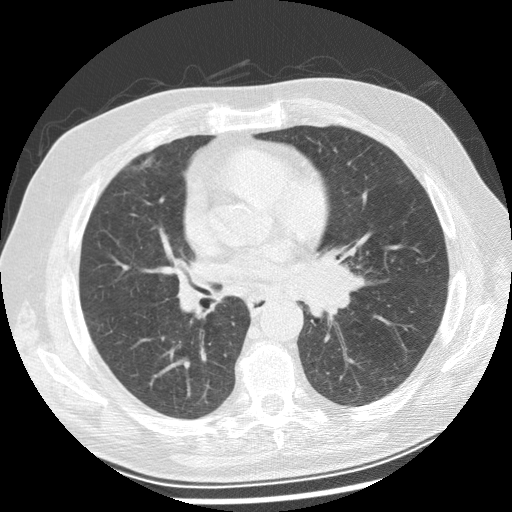
Chest CT (low-dose screening protocol), one axial image; baseline screening round; lung window (W 1500 / L -600 HU); 2.5 mm slice thickness; 120 kVp; slice 120 of 250 in the series. Male participant, aged 70 years at enrolment. Current smoker at enrolment.
Lesion marked by an expert reader, bounding box <291,241,374,322> (left, top, right, bottom; pixels). Screening reader's record for this exam: no non-calcified nodule ≥4 mm recorded. Official screen result: positive, change unspecified: nodule(s) >= 4 mm or enlarging nodule(s), mass(es), or other non-specific abnormalities suspicious for lung cancer.